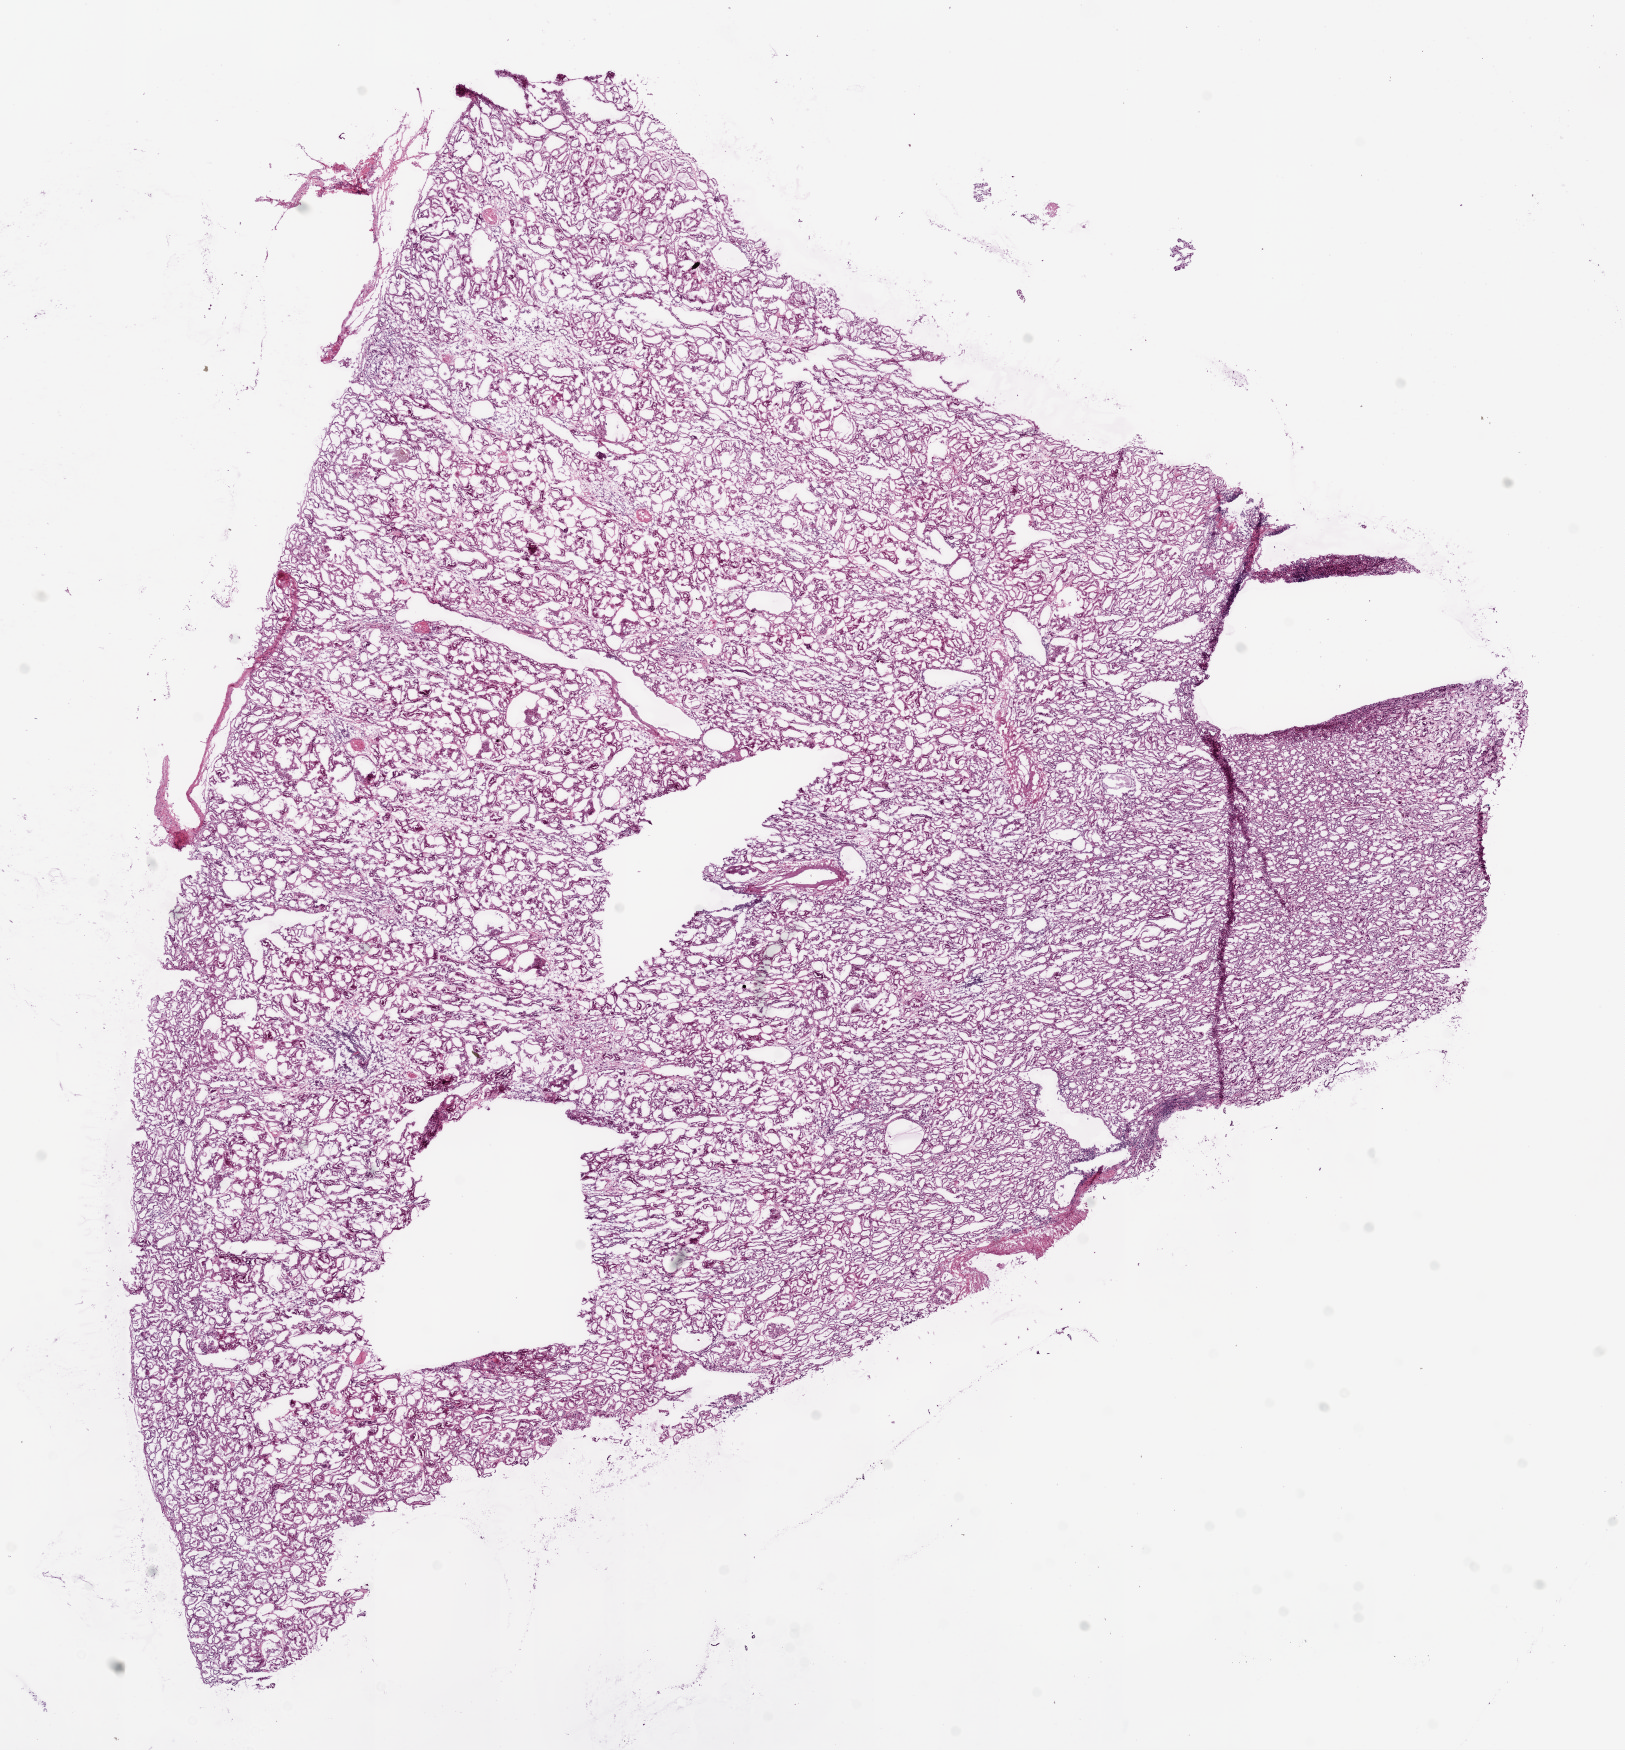
Digitized H&E tissue section (whole slide), a low-resolution overview of the entire scanned area, about 13.0 x 14.0 mm; frozen section; sample: solid tissue normal (non-tumour tissue), kidney. Patient: female, age at initial diagnosis 60 years.
* this section: solid tissue normal (non-tumour) sample from the same patient
* patient diagnosis: Clear cell adenocarcinoma, NOS